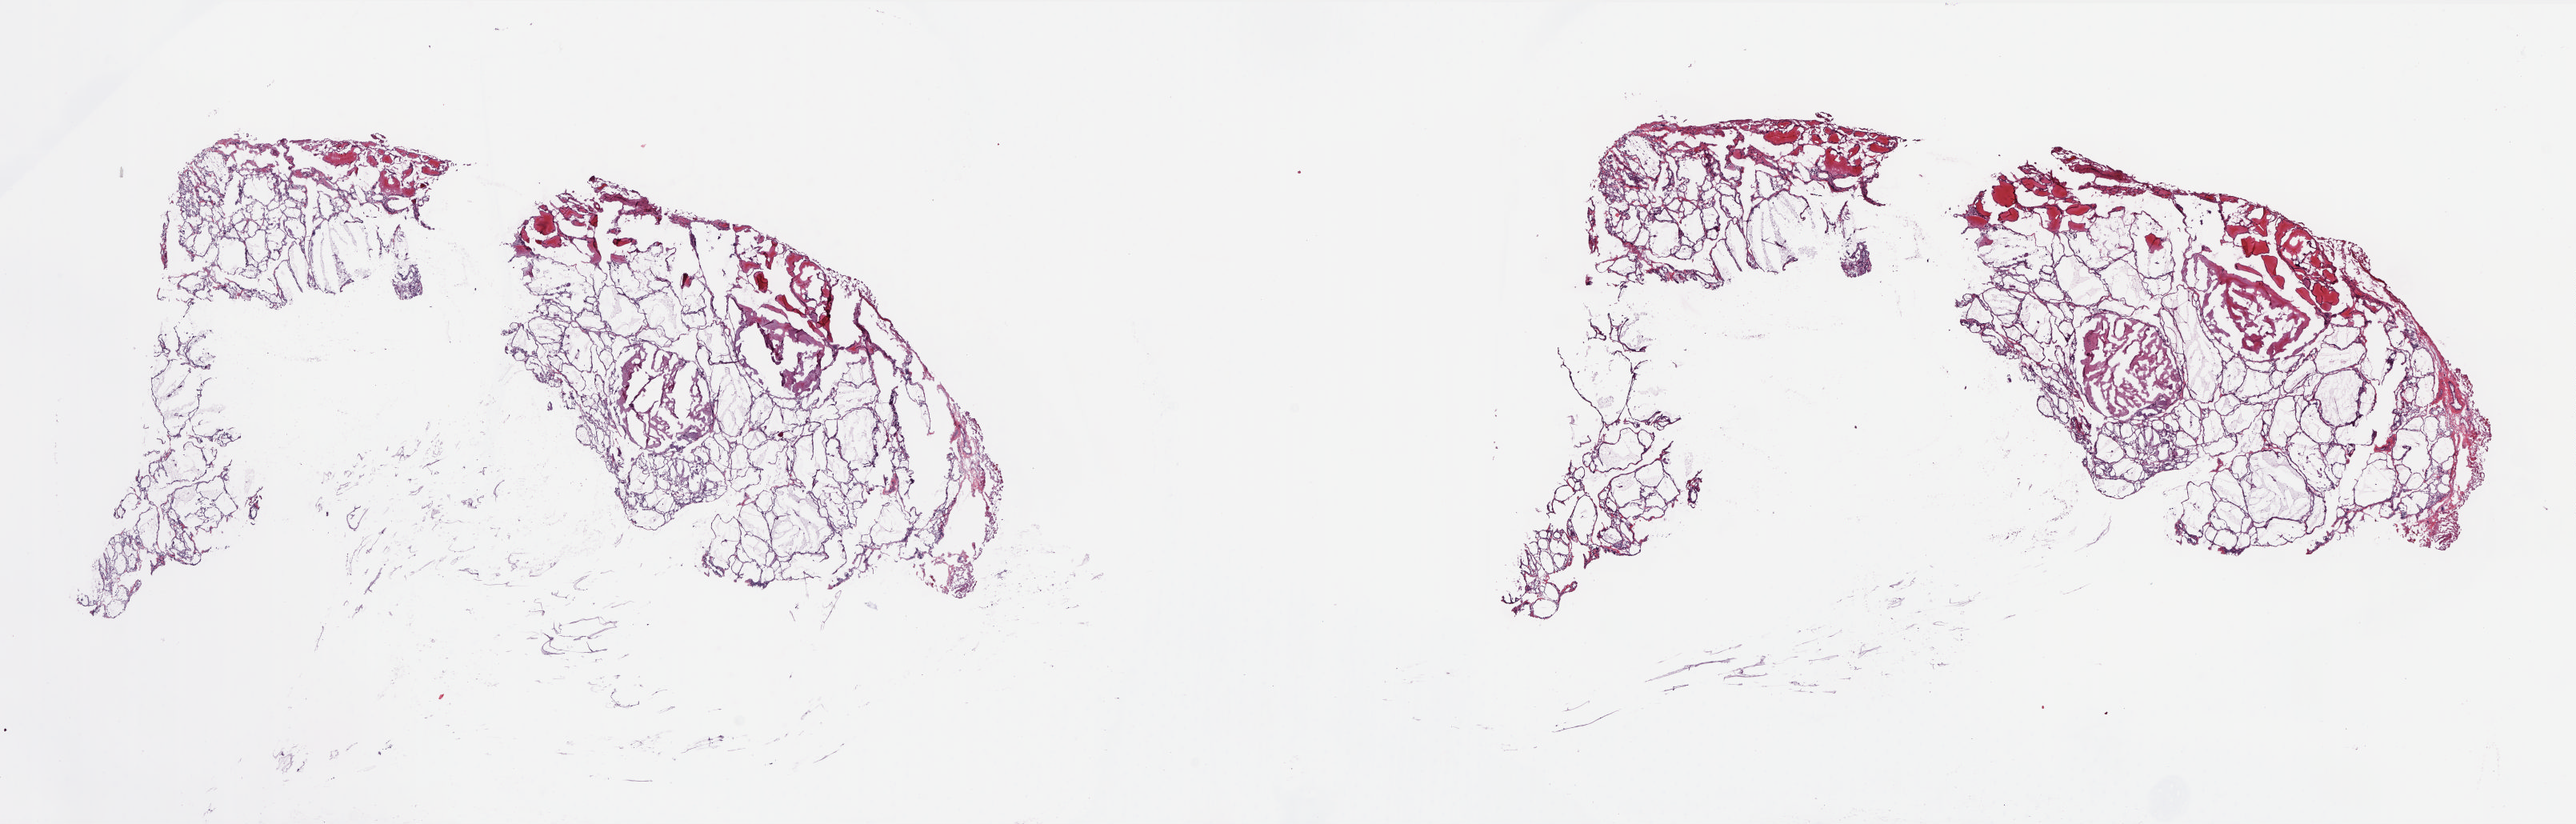
H&E whole-slide image — a low-resolution overview of the entire scanned area, about 26.0 x 8.3 mm, frozen section, sample: solid tissue normal (non-tumour tissue), thyroid. Female, age 33 years at initial diagnosis. Pathologist review of this section (percent, as recorded): tumour cells 0%, tumour nuclei 0%, normal cells 85%, stromal cells 15%, necrosis 0%. Inflammatory infiltration, as recorded: lymphocyte infiltration 4%, monocyte infiltration 2%, neutrophil infiltration 0%.
This section: solid tissue normal sample (biorepository sample class). Patient diagnosis: Papillary adenocarcinoma, NOS (thyroid gland).